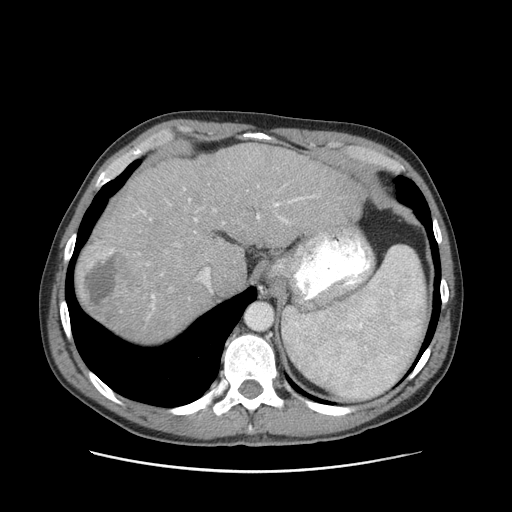
Contrast-enhanced abdominal CT (liver protocol), one axial slice; slice 75 of 93 in the series (ordered by position); 120 kVp; soft-tissue window (W 400 / L 40 HU); 512 × 512 image matrix. Case-level facts recorded for this patient, not image findings: diagnosis: hepatocellular carcinoma (patient treated with transarterial chemoembolisation; whether this scan precedes or follows treatment is not stated here); TNM stage (as recorded): Stage-II; Child-Pugh class: A; tumour differentiation: moderately differentiated.
Outlined on this slice (semi-automatic segmentation, software-assisted and operator-edited):
- abdominal aorta: box from (x=246, y=304) to (x=272, y=329) px
- liver parenchyma outside the tumour (the mass and vessels are separate outlines, so this box may not span the whole liver): (x=76, y=144)–(x=364, y=342)
- mass: (x=81, y=247)–(x=145, y=321)
- liver vessels: (x=141, y=188)–(x=314, y=307)